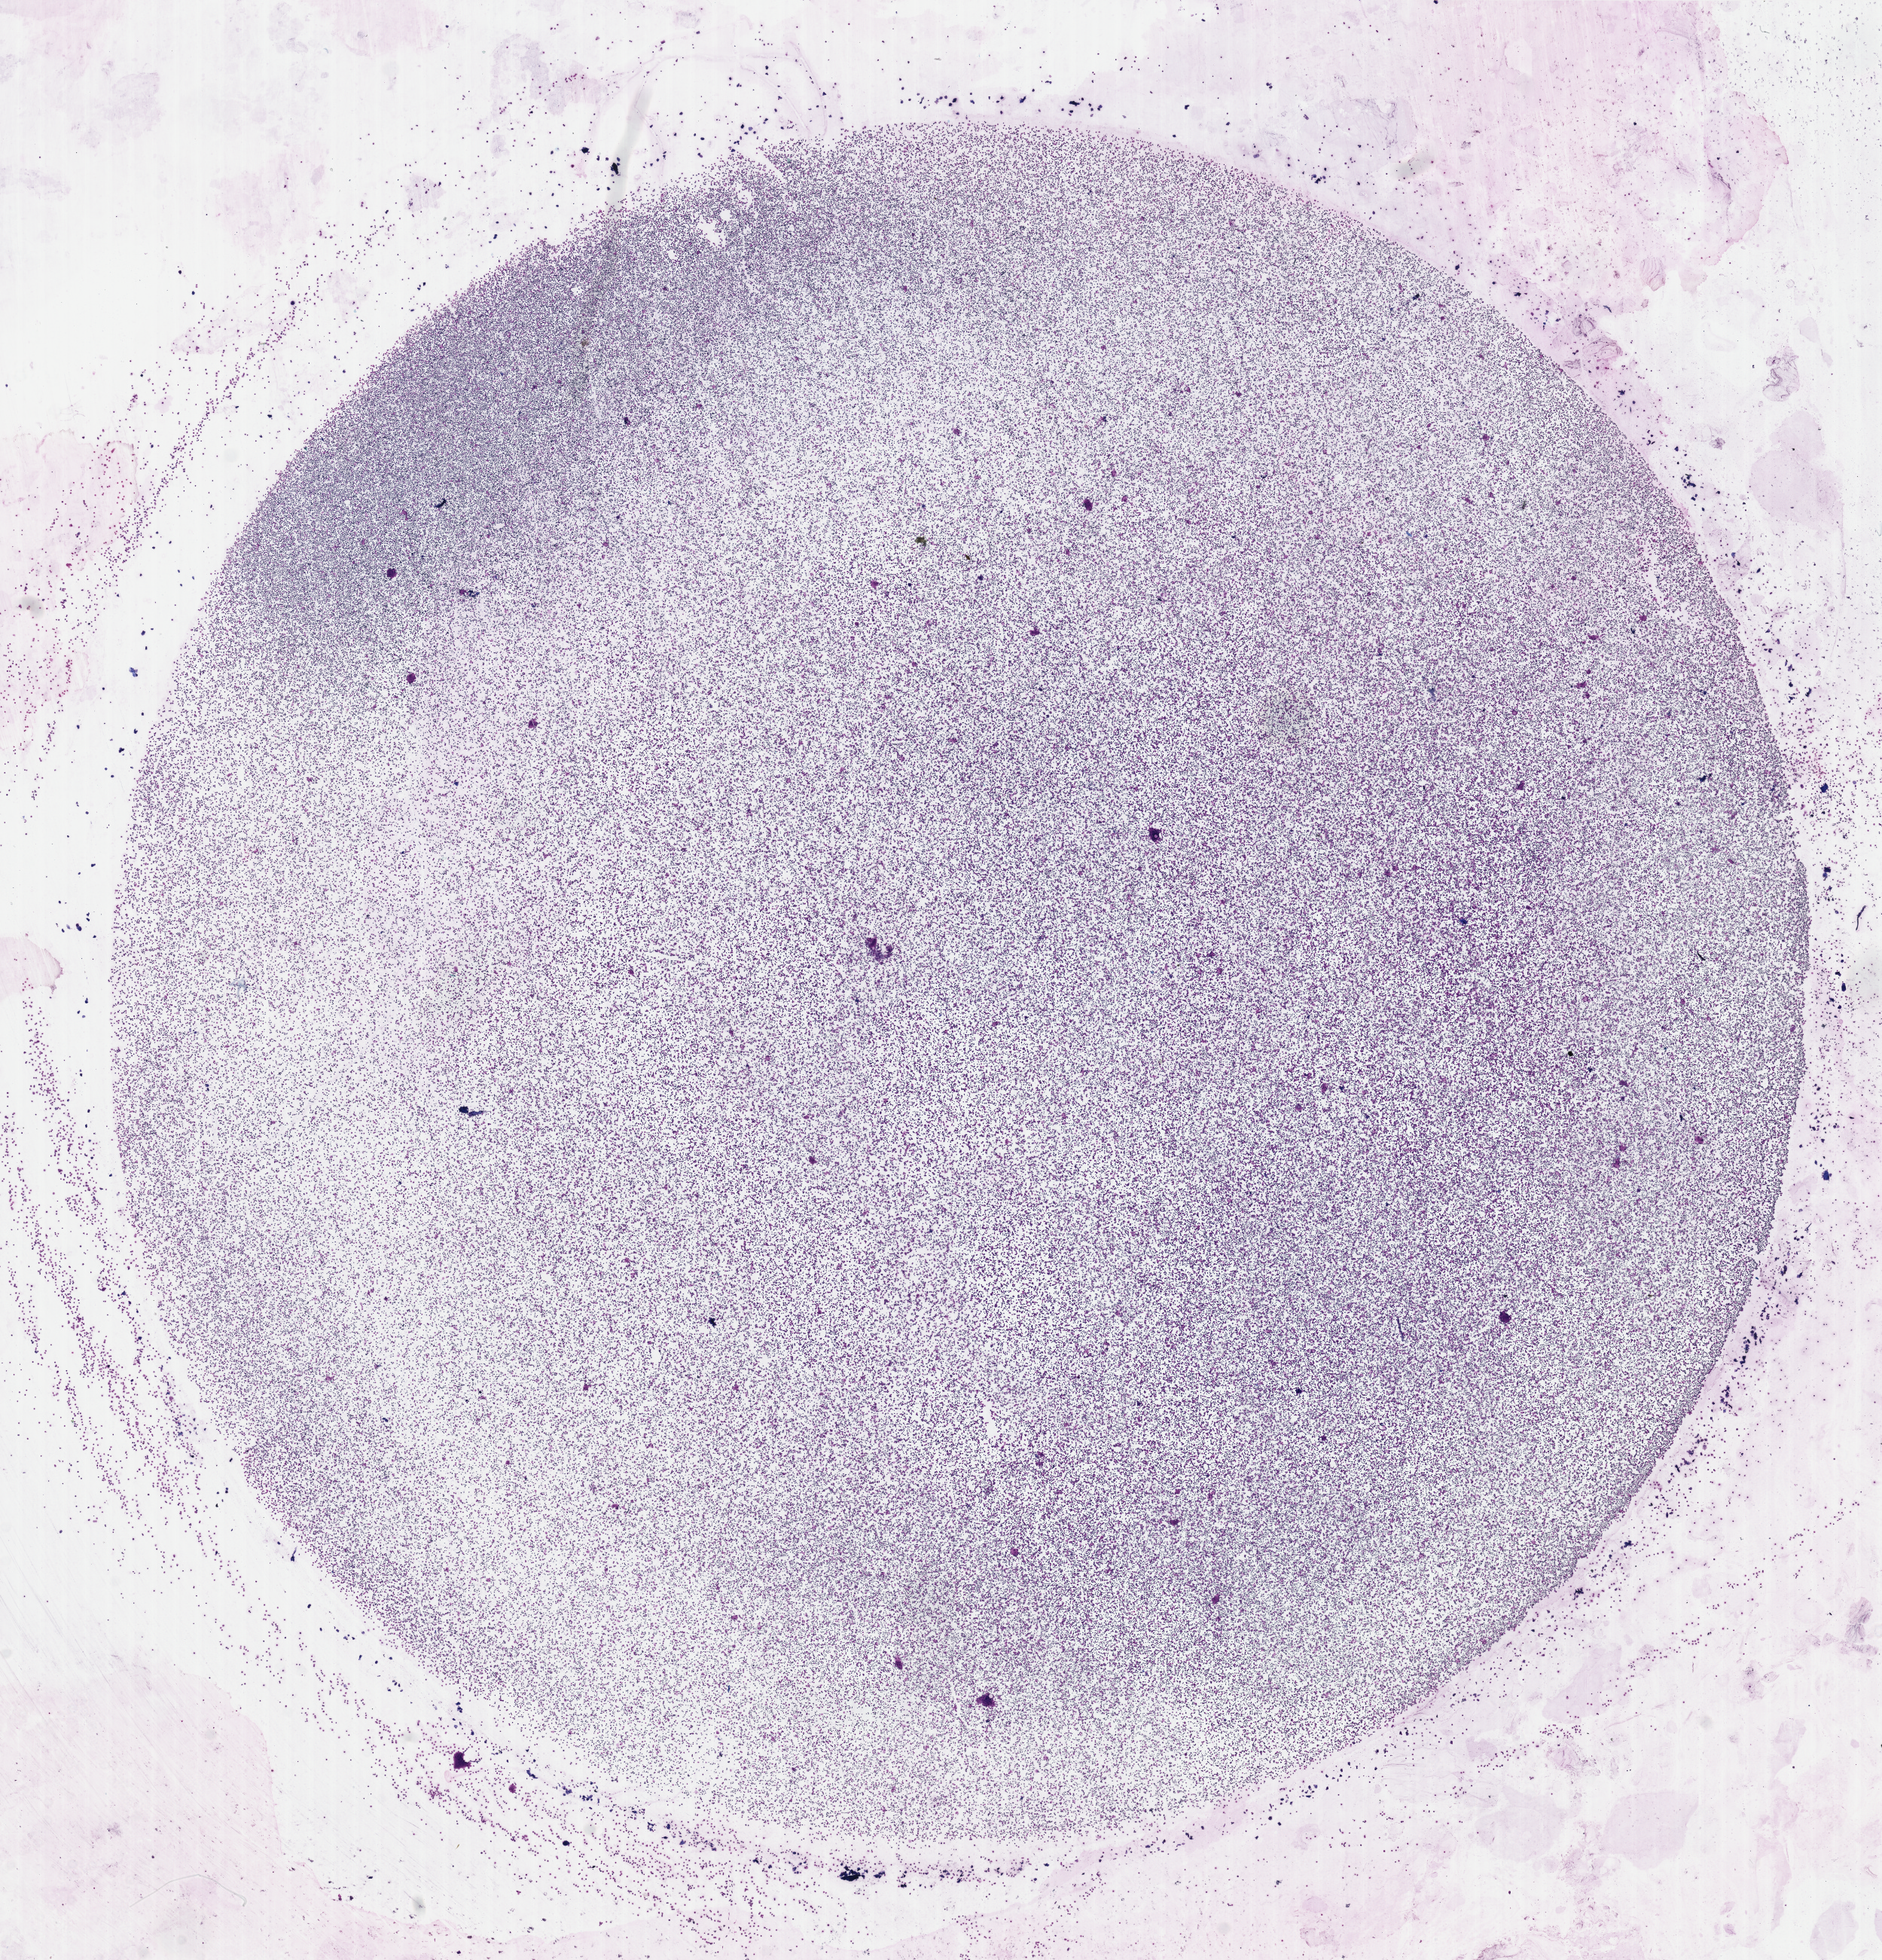
Whole-slide histology image, H&E-stained — whole scanned area (about 19.7 x 20.5 mm, acquisition: 40x scan) shown as a low-resolution overview; bone marrow (leukaemic) sample. 70-year-old male patient. Blasts: 90%.
FAB classification: M4. WHO classification: Acute myelomonocytic leukemia. Diagnosis: Acute Myeloid Leukemia.